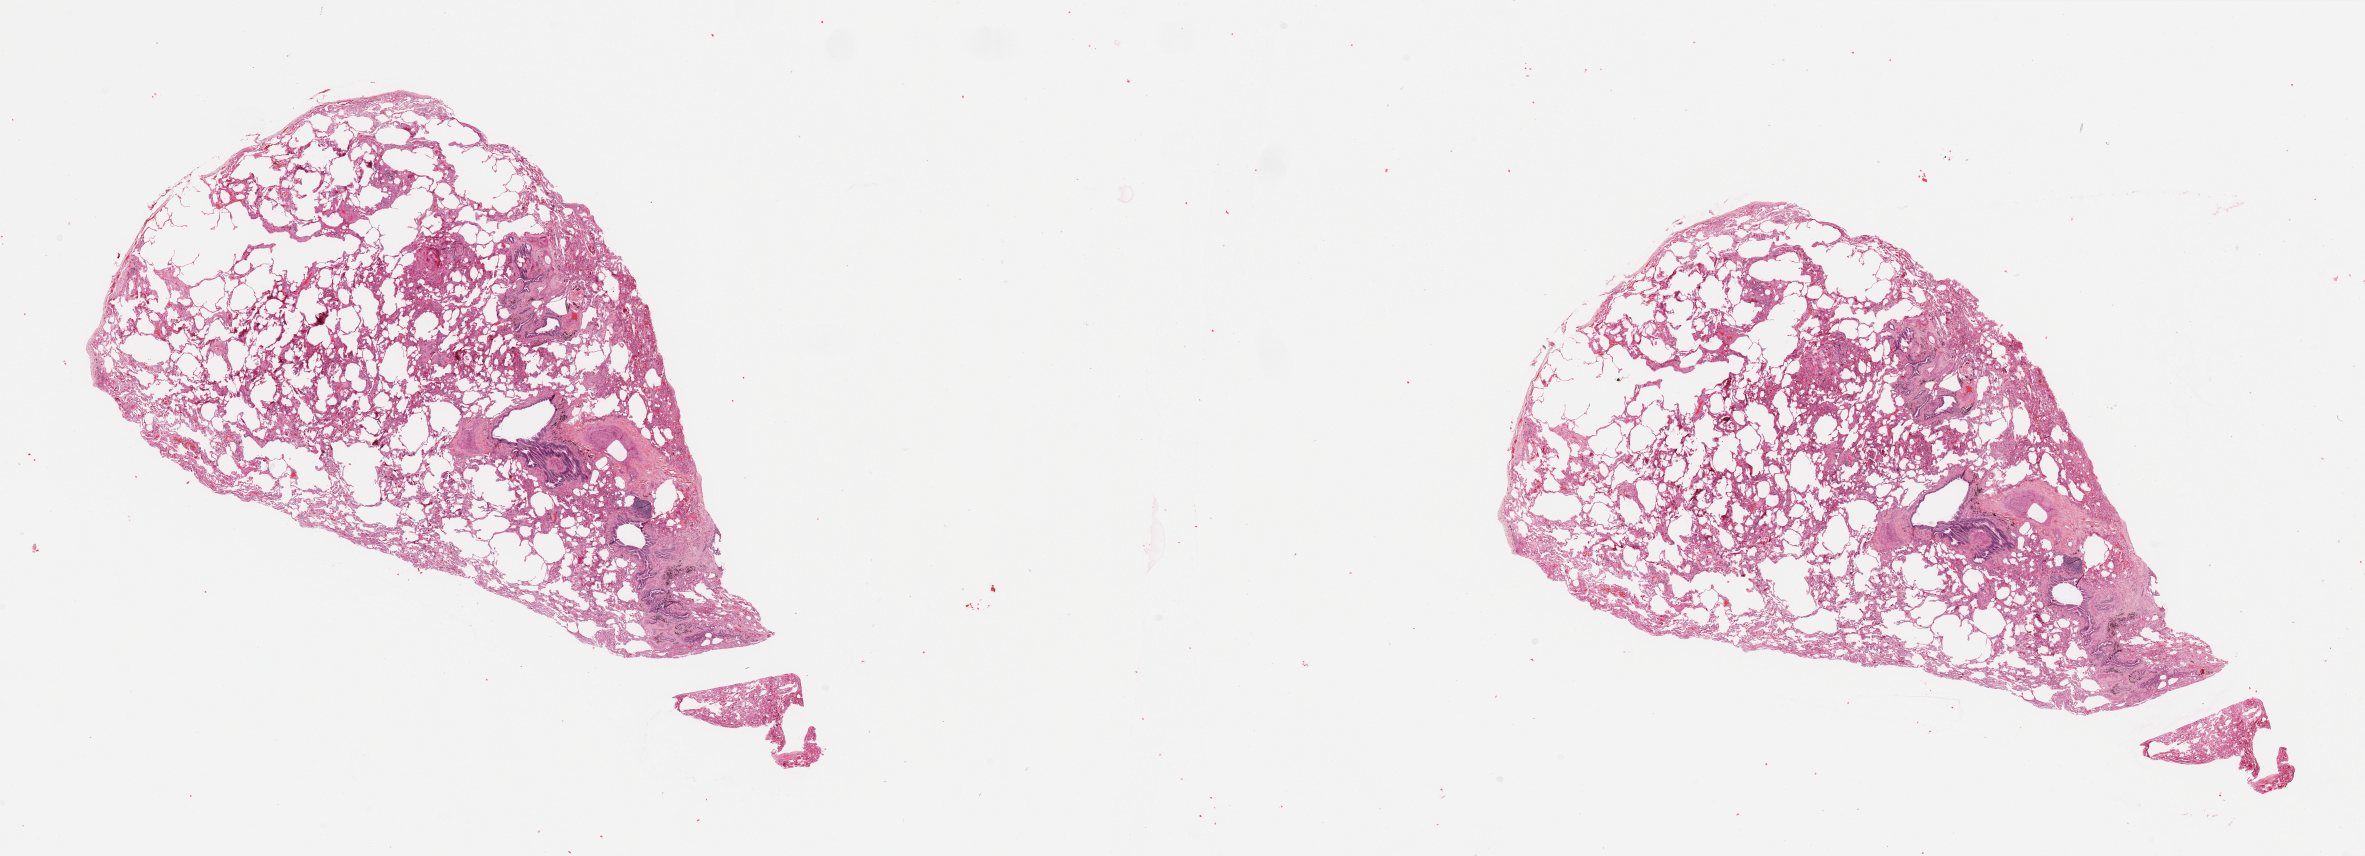
H&E-stained whole-slide image — whole scanned area (about 37.4 x 13.5 mm) shown as a low-resolution overview; normal (non-tumour) tissue sample, lung. Patient: female, age 69 years.
This section: normal (non-tumour) tissue from the same patient. Patient diagnosis: Adenocarcinoma, NOS.